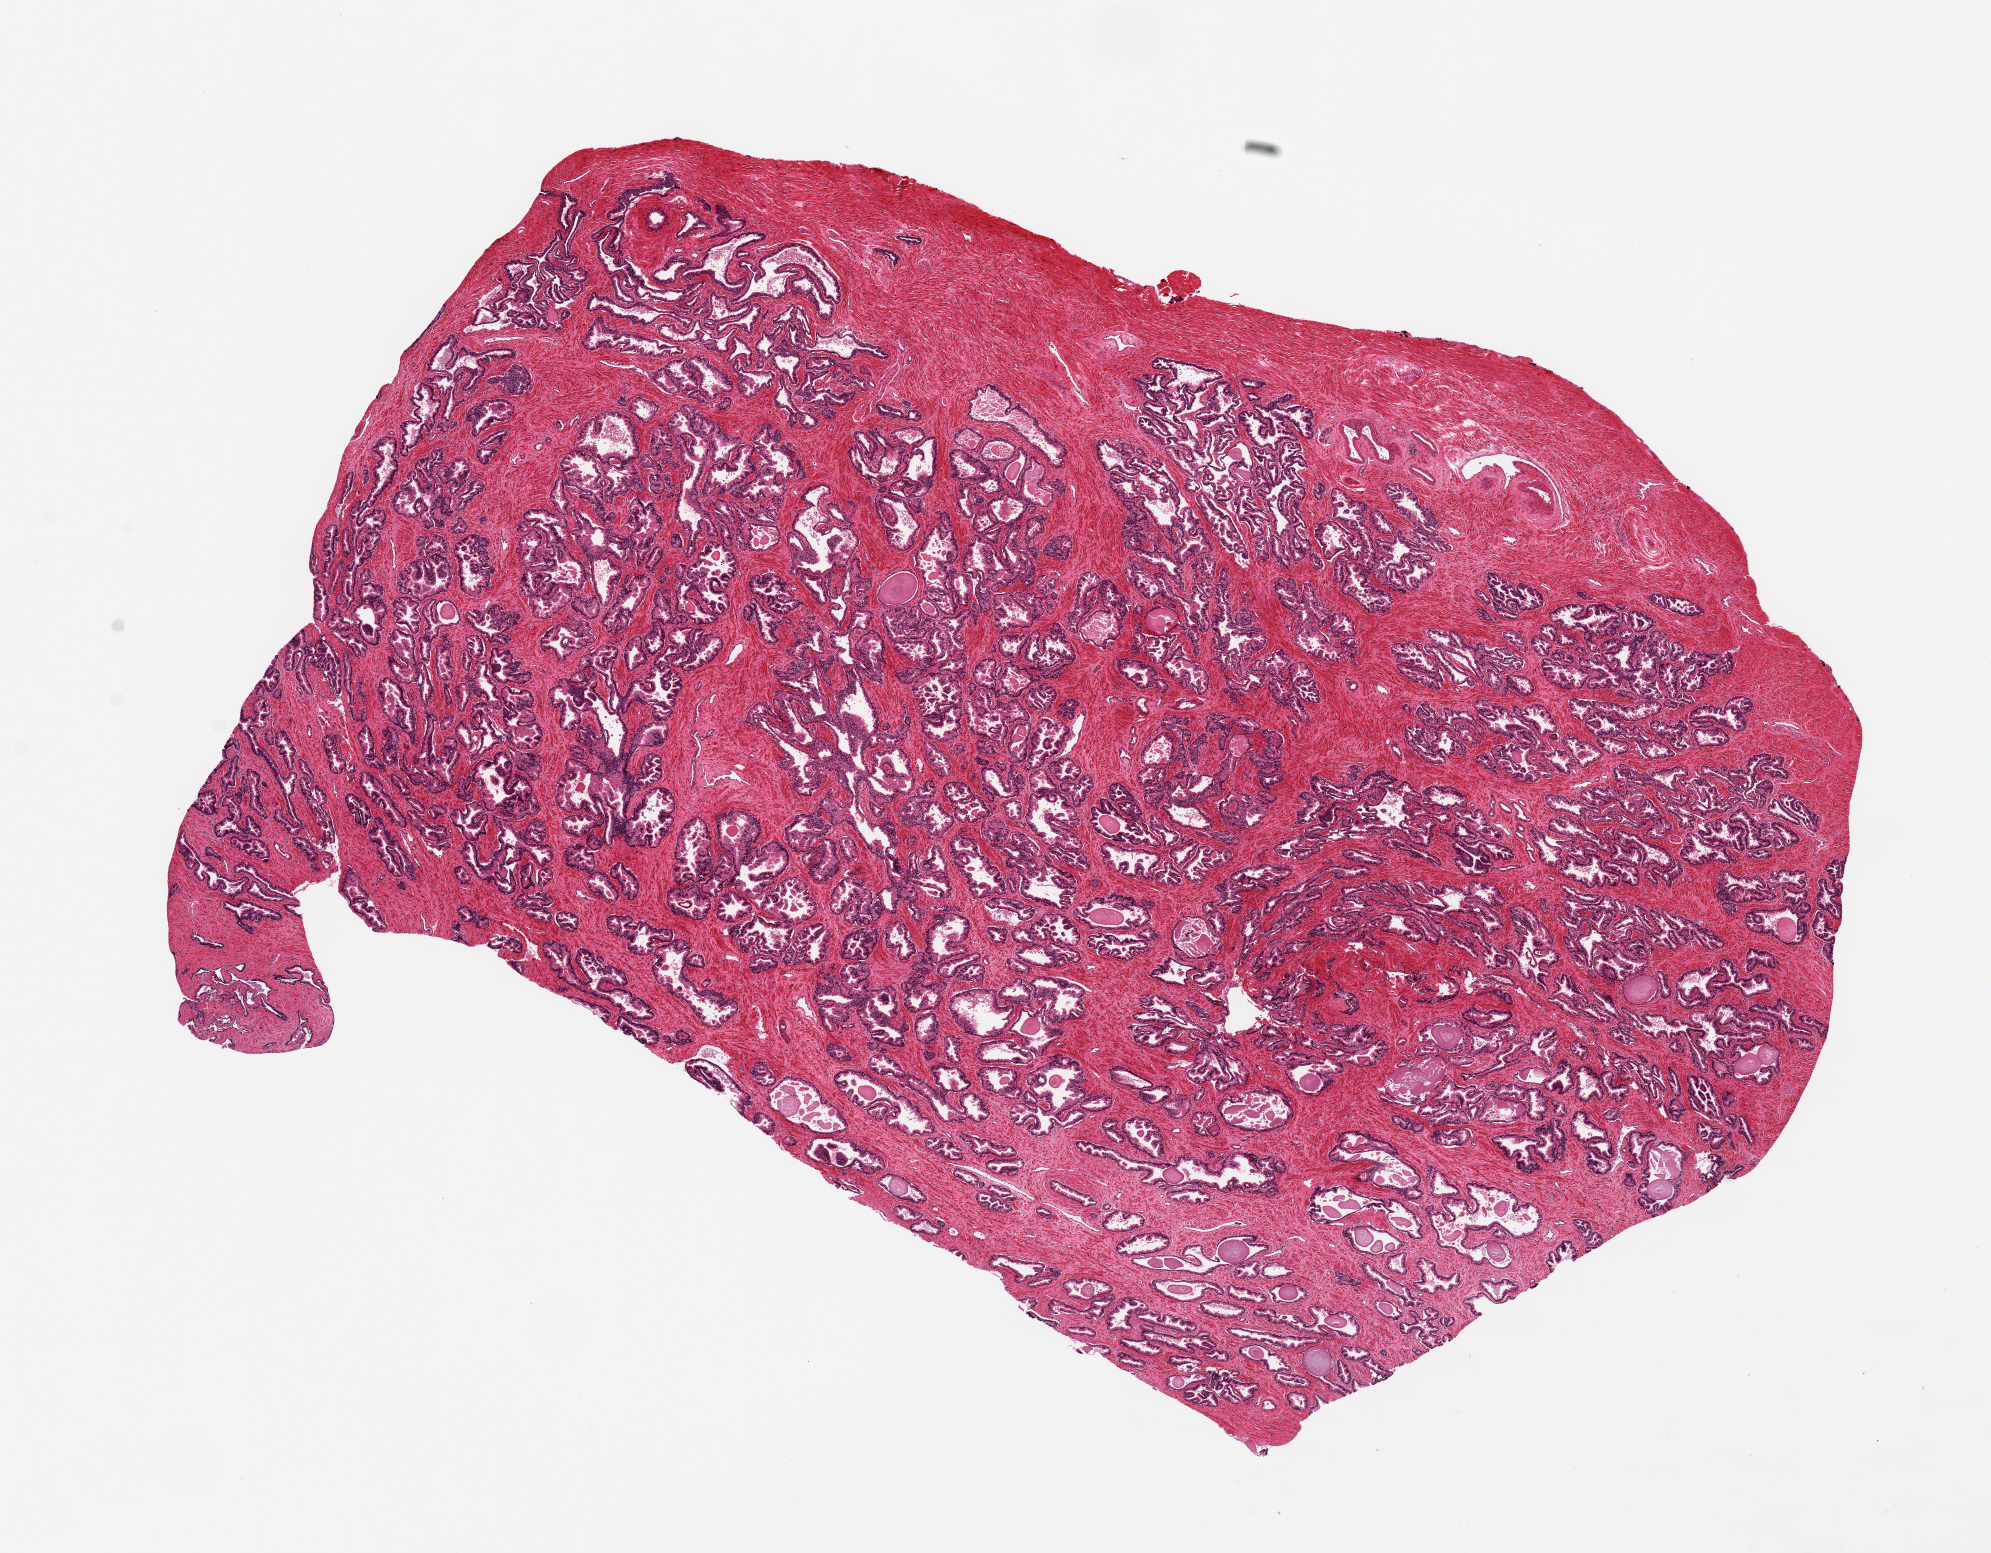
Digitized hematoxylin and eosin (H&E)-stained section, brightfield, whole scanned area (about 15.8 x 12.3 mm) shown as a low-resolution overview, PAXgene-fixed paraffin-embedded (PFPE) section, section of prostate (target tissue), donor tissue sample. Donor: male.
Reviewer comment on this tissue sample: 1. 12 x 8.2mm. Mild glandular hyperplasia.